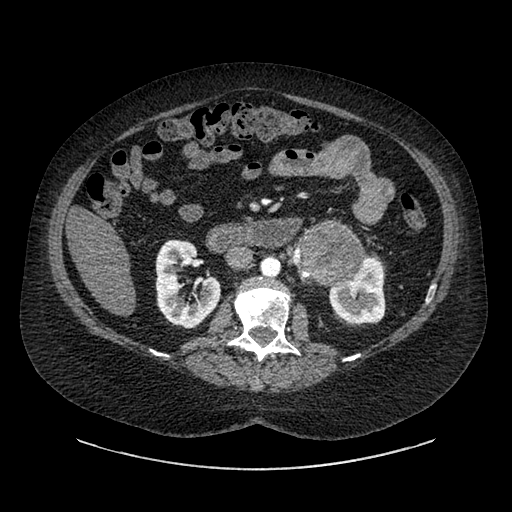
Contrast-enhanced abdominal CT, one axial slice; position 505 of 769 along the scan axis; intravenous contrast given; soft-tissue window (W 400 / L 40 HU); 0.62 mm slice thickness; 512 × 512 image matrix. Patient: female, 61 years. From the clinical record (not read from this slice): diagnosis: adrenocortical carcinoma; tumour side: left adrenal; tumour size at pathology: 13 cm; Ki-67 index: 79 %; stage (as recorded): 2.
Structures marked on this image (semi-automatically segmented with operator editing):
- mass: bounding box (x1, y1, x2, y2) in pixels: (297, 225, 362, 281)